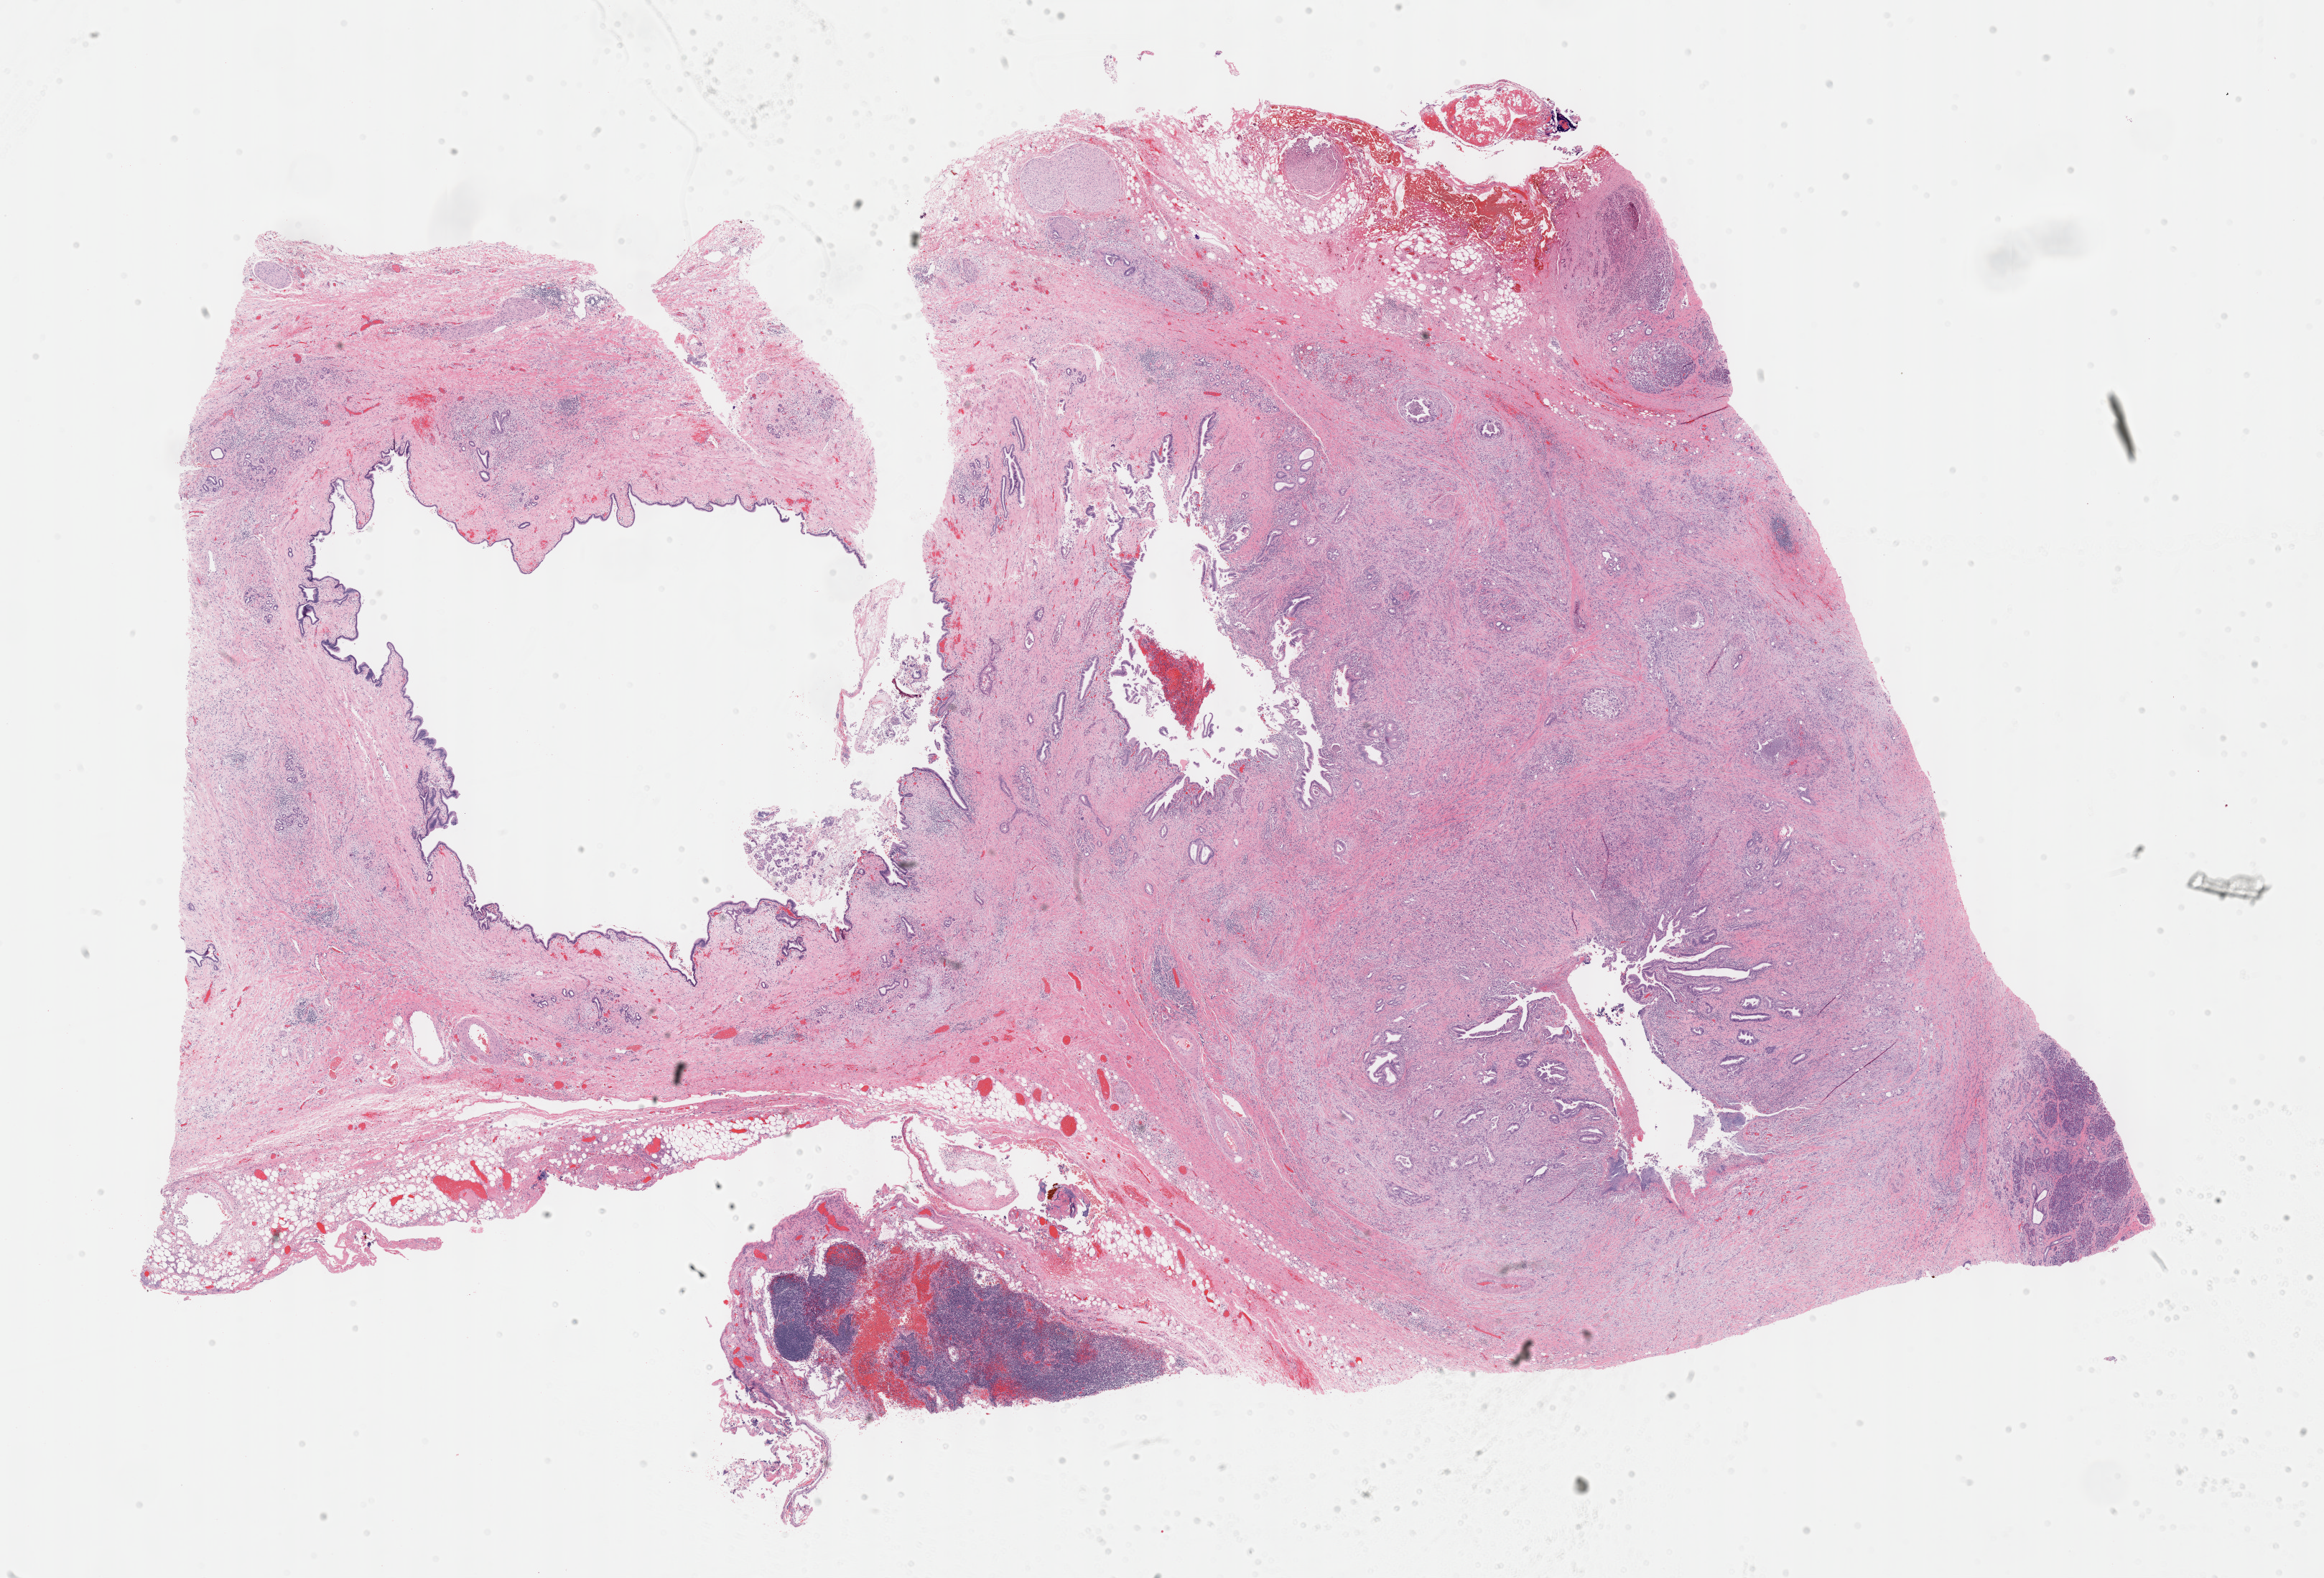
Digitized H&E-stained tissue section (whole slide), low-resolution overview of the scanned area, about 26.2 x 17.8 mm. Formalin-fixed paraffin-embedded (FFPE) diagnostic section. Pancreas, primary tumour sample. Female, age 50 years at initial diagnosis. Histologic grade: G2 (moderately differentiated).
• AJCC pathologic stage: IIB (7th edition)
• TNM: T3 N1 MX
• lymph nodes positive (case pathology): 10 of 33 examined
• diagnosis: Infiltrating duct carcinoma, NOS